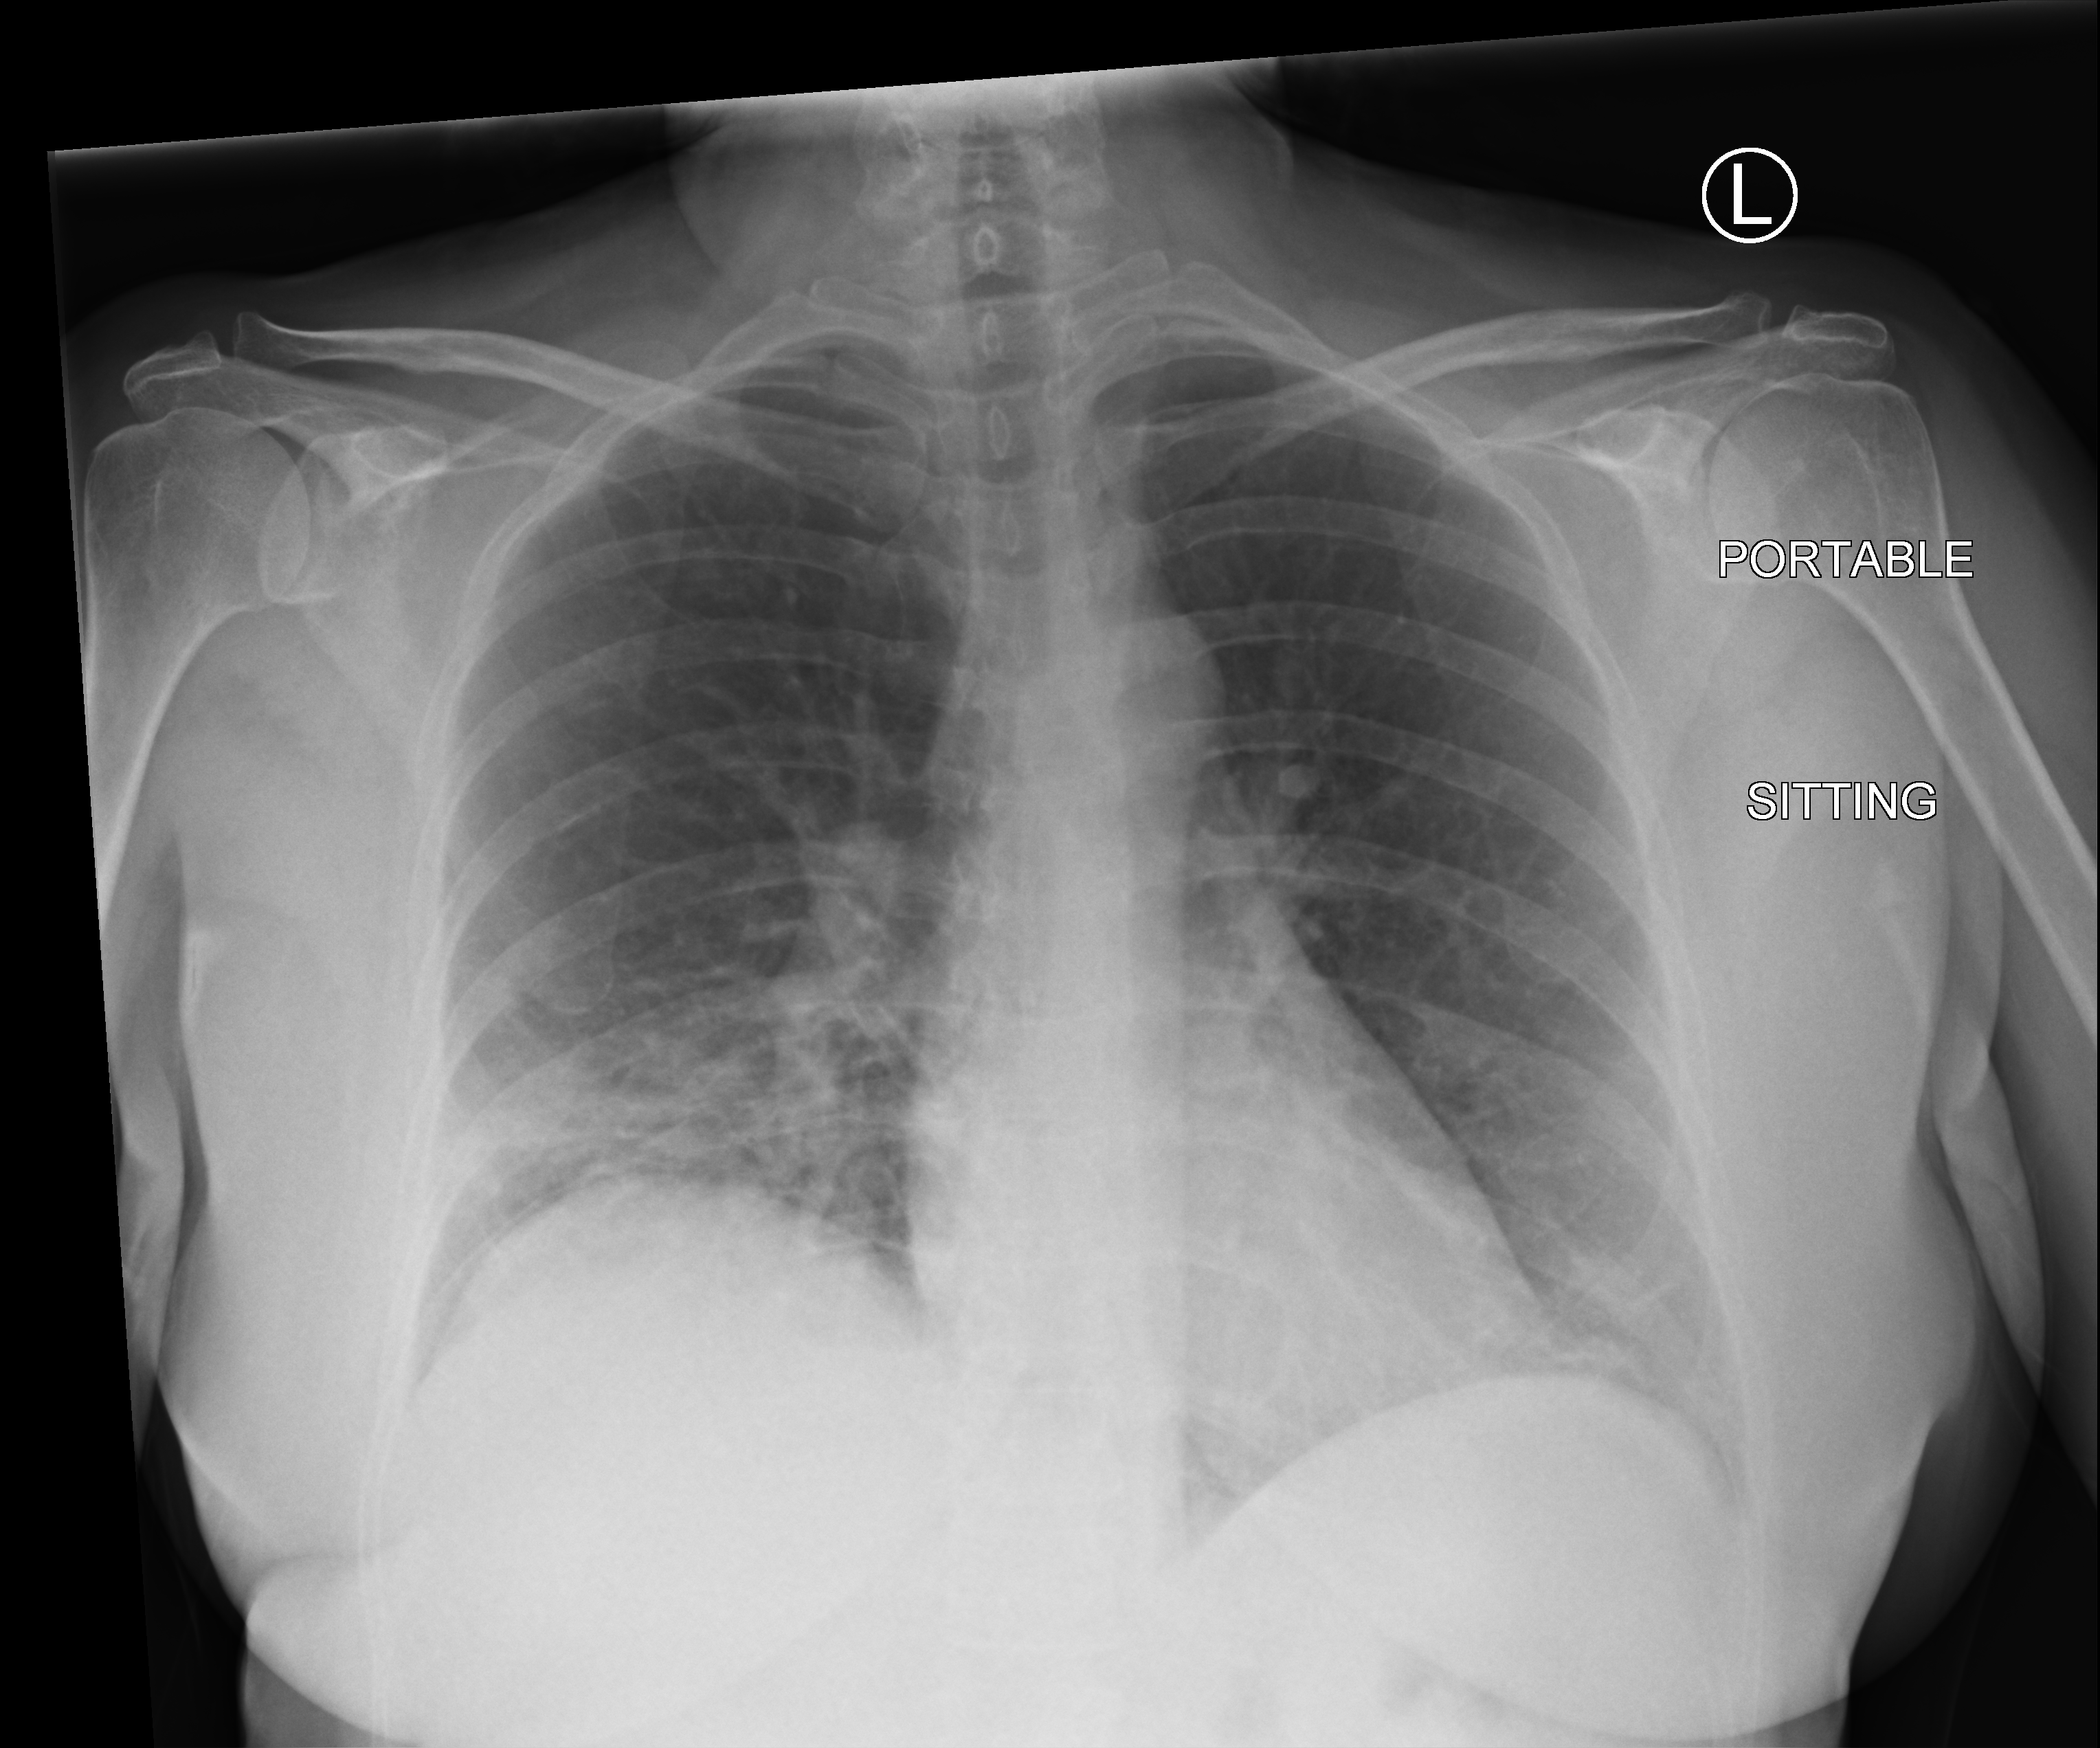
Bedside chest radiograph (computed radiography), anteroposterior (AP) projection. Female patient hospitalised with COVID-19, age 18–59 years.
Hospital-stay facts (about this admission, not read from this image; timing relative to this image not recorded): admitted to intensive care during this hospital stay: no; smoking status (admission record): never; mechanically ventilated during this hospital stay: no.